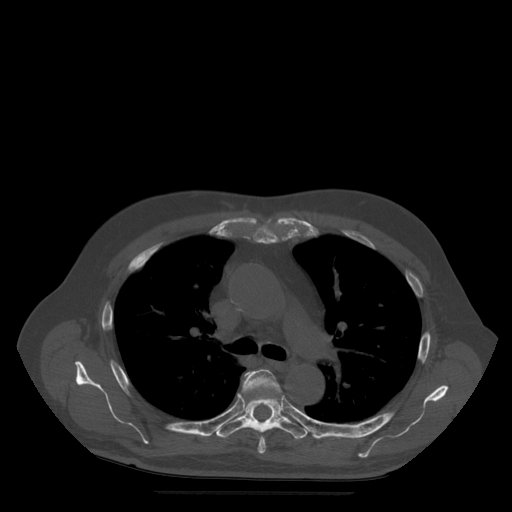
CT including the spine, one axial slice. Slice 361 of 522 in the series (ordered by position). Bone window (W 1800 / L 400 HU). 1.25 mm slice thickness. 512 × 512 image matrix. Patient age 72 years. From the clinical record (not read from this slice): primary cancer: prostate.
Structures marked on this image (semi-automatic segmentation, software-assisted and operator-edited):
- T5 vertebra: bounding box (x1, y1, x2, y2) in pixels: (243, 369, 281, 454)
- T6 vertebra: (217, 372, 308, 440)